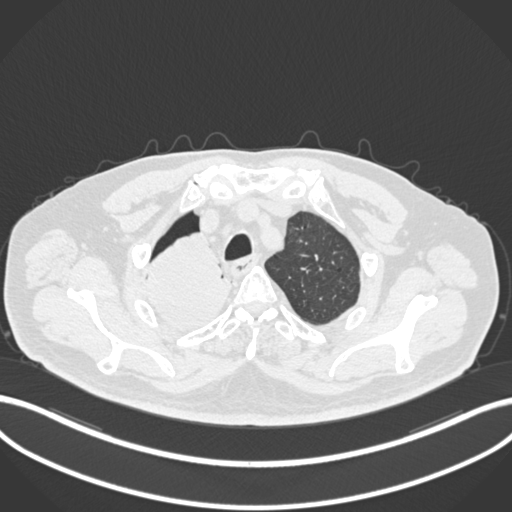
Chest CT, one axial slice. Position 179 of 218 along the scan axis. Reconstruction kernel B30f. Lung window (W 1500 / L -600 HU). 512 × 512 image matrix, field of view 400 × 400 mm. Patient: male, 68 years. Case-level facts recorded for this patient, not image findings: clinical TNM (as recorded): T2a N0 M0.
Structures marked on this image (rectangle marked by the reading radiologist):
- lung tumour (recorded histology: adenocarcinoma): bounding box [x1, y1, x2, y2] px = [143, 230, 231, 331]